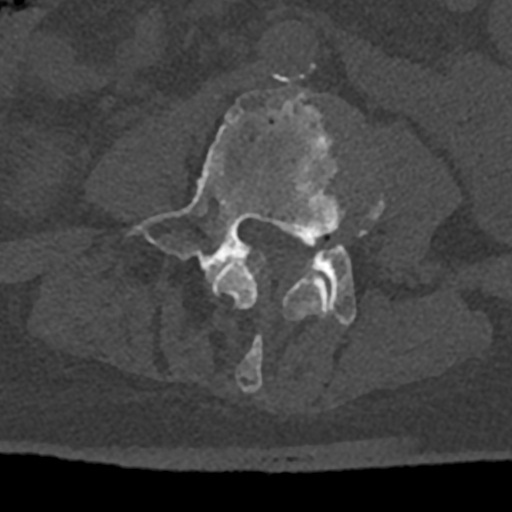
CT including the spine, one axial slice. Position 279 of 797 along the scan axis. 120 kVp. Bone window (W 1800 / L 400 HU). 0.5 mm slice thickness. 512 × 512 image matrix, field of view 160 × 160 mm. Male patient, age 74 years. From the clinical record (not read from this slice): primary cancer: renal; vertebrae with lytic lesions (as recorded): T10, L1, L2, L3, L4, L5.
Annotated regions visible in this slice (semi-automatic segmentation, software-assisted and operator-edited):
- L3 vertebra: bounding box (x1, y1, x2, y2) in pixels: (212, 180, 384, 392)
- L4 vertebra: (131, 87, 356, 326)